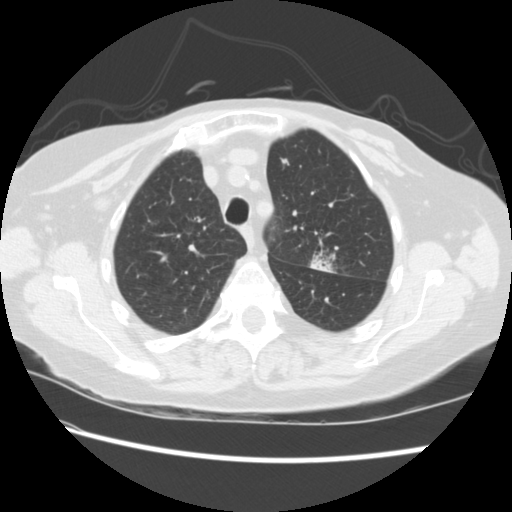
Axial slice from a low-dose chest CT screening exam, baseline screening round, lung window (W 1500 / L -600 HU), standard (soft-tissue) reconstruction kernel (STANDARD), 120 kVp, 512 × 512 image matrix. Female, age 74 years at enrolment. Former smoker at enrolment.
• Expert reader's lesion annotation, bounding box [x1, y1, x2, y2] px = [296, 236, 346, 279].
• The screening reader recorded 2 non-calcified nodules or masses ≥4 mm on this exam; which of them this box marks is not recorded.
• Official screen result: positive, change unspecified: nodule(s) >= 4 mm or enlarging nodule(s), mass(es), or other non-specific abnormalities suspicious for lung cancer.
• Participant outcome: lung cancer diagnosed 309 days after this screen — non-small cell carcinoma, left upper lobe, stage IV (AJCC 6th edition).